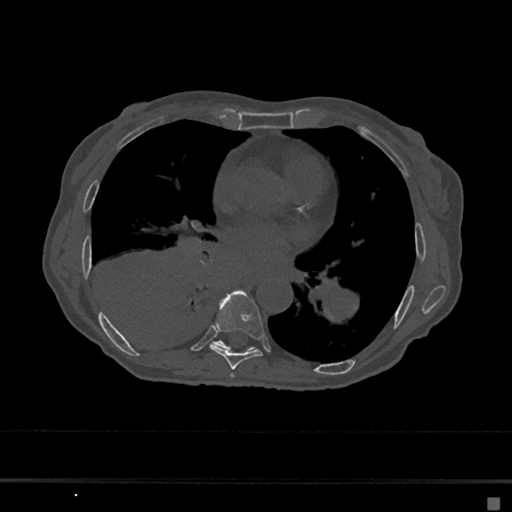
CT including the spine, one axial slice. Reconstruction kernel Br40s/3. 120 kVp. Bone window (W 1800 / L 400 HU). 512 × 512 image matrix, field of view 360 × 360 mm. Female patient, age 68 years. From the clinical record (not read from this slice): primary cancer: renal.
Structures marked on this image (semi-automatic segmentation, software-assisted and operator-edited):
- T6 vertebra: bounding box (x1, y1, x2, y2) in pixels: (230, 374, 234, 379)
- T7 vertebra: (210, 291, 264, 370)
- T8 vertebra: (213, 340, 255, 351)